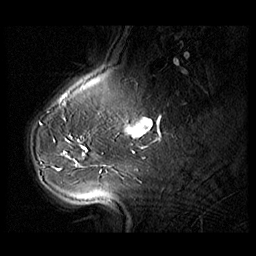
Breast MRI (dynamic contrast-enhanced), one sagittal slice; position 27 of 104 along the scan axis; 3 images stored at this slice position (order not interpretable as contrast timing); 1.5 T; TE 1.3 ms, TR 5.5 ms; 256 × 256 image matrix, field of view 220 × 220 mm. Female patient, age 54 years. Case-level facts recorded for this patient, not image findings: setting: breast cancer imaged before/during neoadjuvant chemotherapy; receptor status: HR-positive, HER2-negative.
Outlined on this slice (semi-automatic segmentation, software-assisted and operator-edited):
- analysis volume of interest (the breast-tissue region the enhancement analysis was run in; not a lesion): box from (x=28, y=127) to (x=104, y=182) px
- tumour enhancement mask (voxels above the 140 % enhancement threshold inside the analysis volume of interest): (x=63, y=145)–(x=86, y=155)